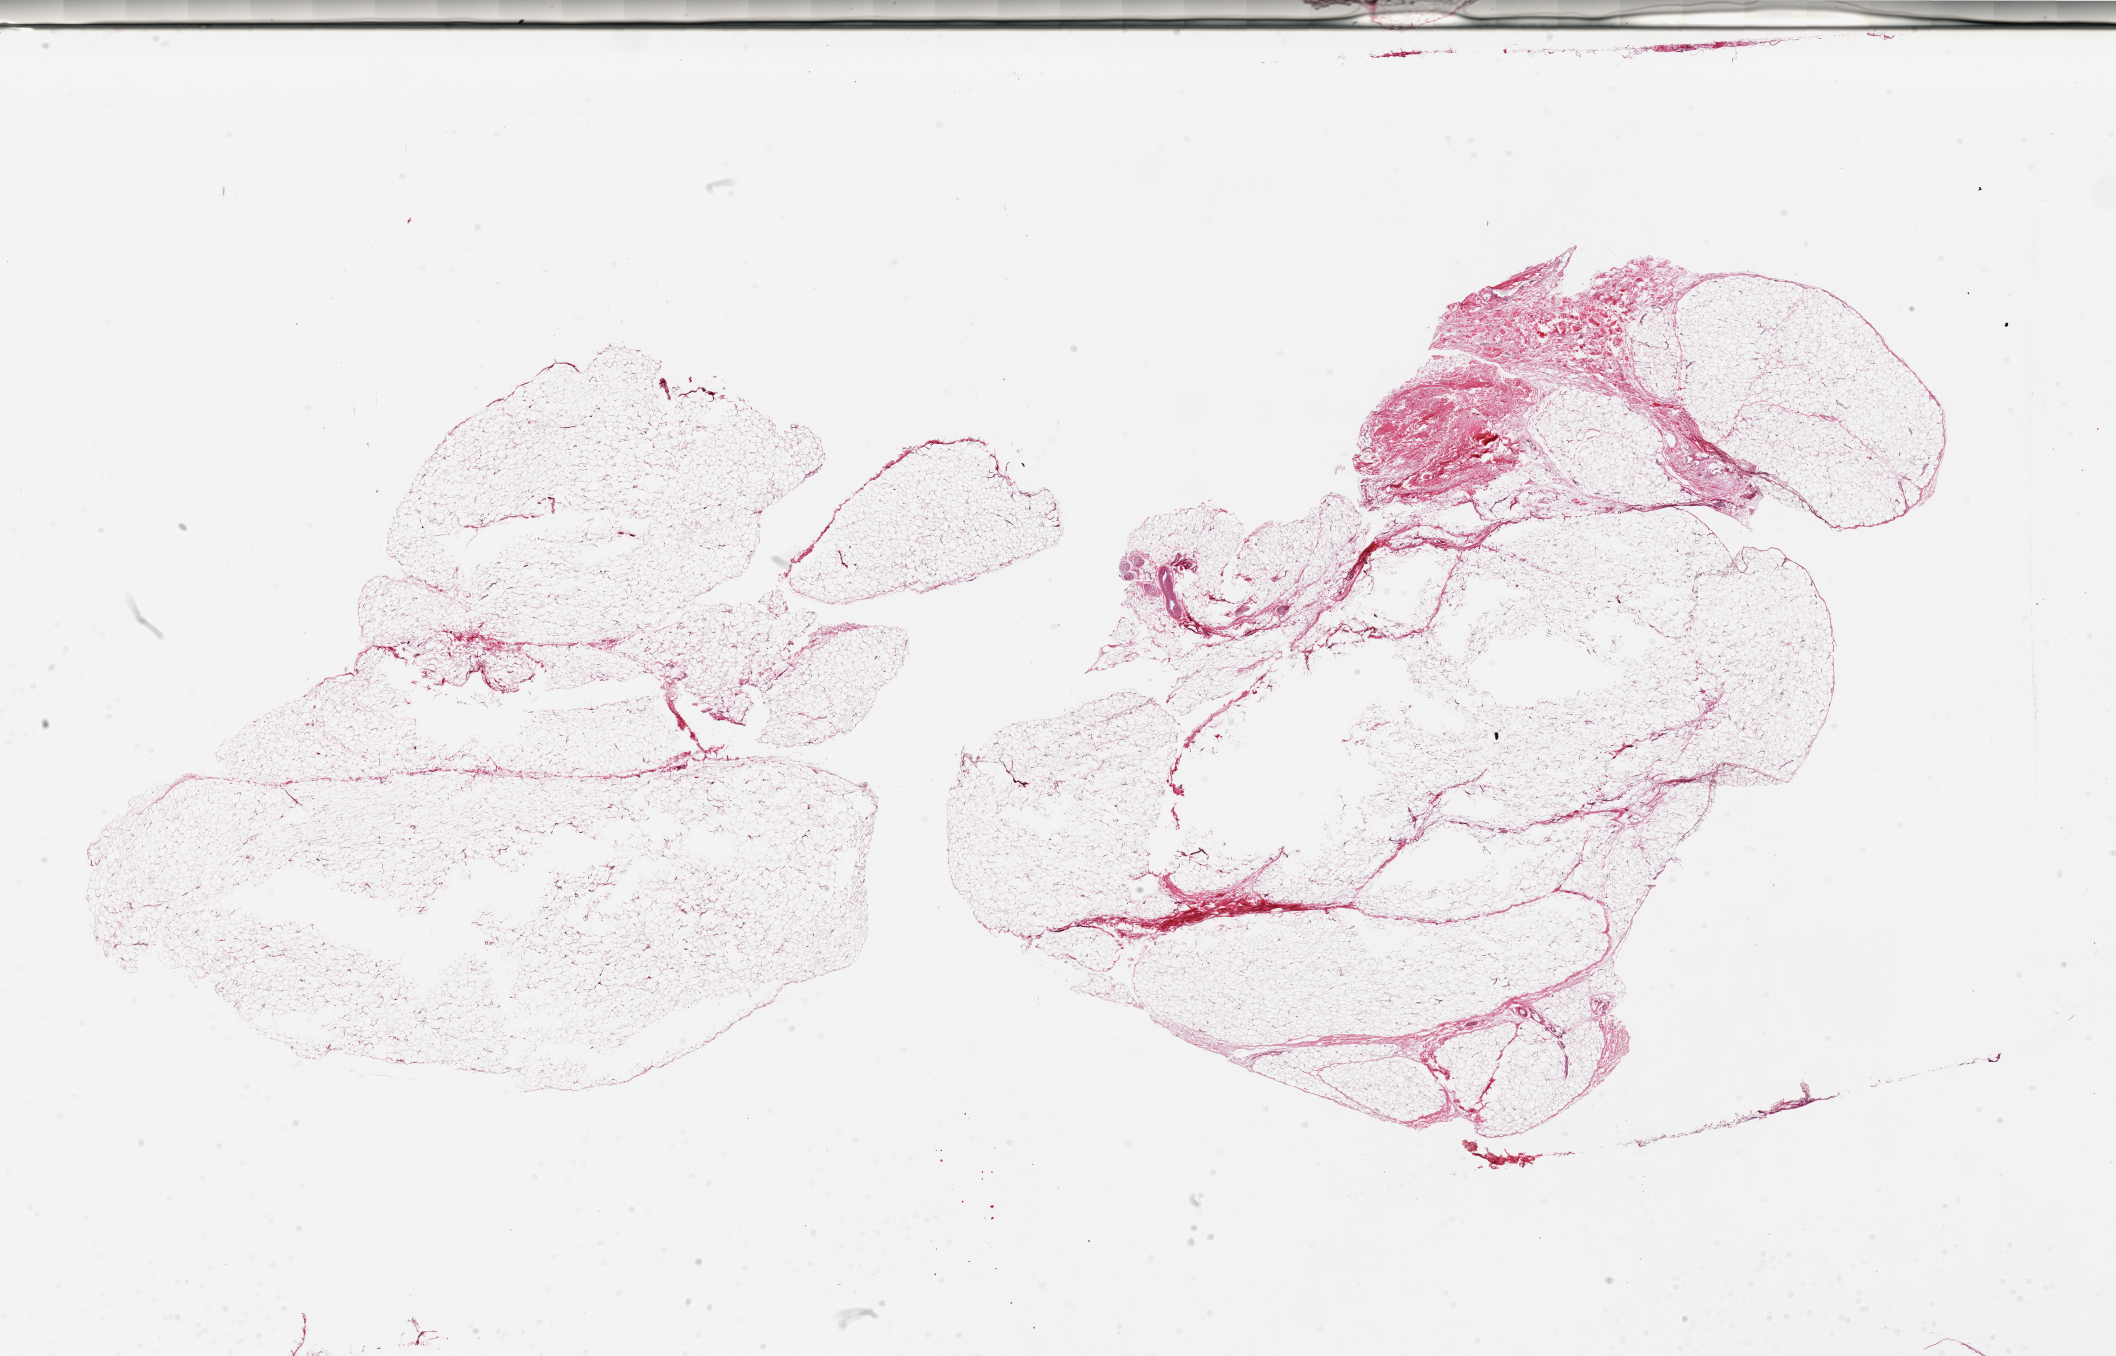
Digitized hematoxylin and eosin (H&E)-stained section — low-resolution overview of the scanned area, about 33.5 x 21.4 mm, PAXgene-fixed paraffin-embedded (PFPE) section, target tissue: adipose tissue, donor tissue sample. Female donor.
* review note (as recorded): 2 pieces; 10% fibrous content in 1 piece